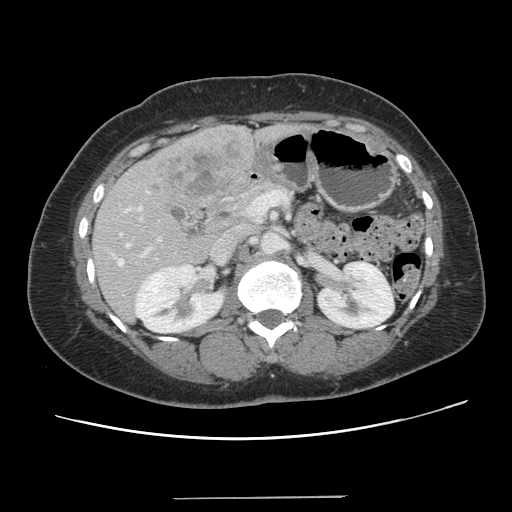
Contrast-enhanced abdominal CT, one axial slice; slice 62 of 141 in the series (ordered by position); 120 kVp; intravenous contrast given; soft-tissue window (W 400 / L 40 HU); 2.5 mm slice thickness; 512 × 512 image matrix, field of view 366 × 366 mm. Female patient, age 53 years. Case-level facts recorded for this patient, not image findings: diagnosis: colorectal cancer liver metastases, imaged before liver resection; multiple liver metastases: no; largest metastasis: 14.5 cm.
Outlined on this slice (expert manual segmentation):
- hepatic veins: box from (x=117, y=243) to (x=129, y=265) px
- liver: (x=92, y=125)–(x=263, y=321)
- planned liver remnant (the part of the liver to remain after resection): (x=92, y=214)–(x=213, y=322)
- portal vein (with intrahepatic branches): (x=138, y=207)–(x=159, y=254)
- liver metastasis: (x=151, y=141)–(x=244, y=198)